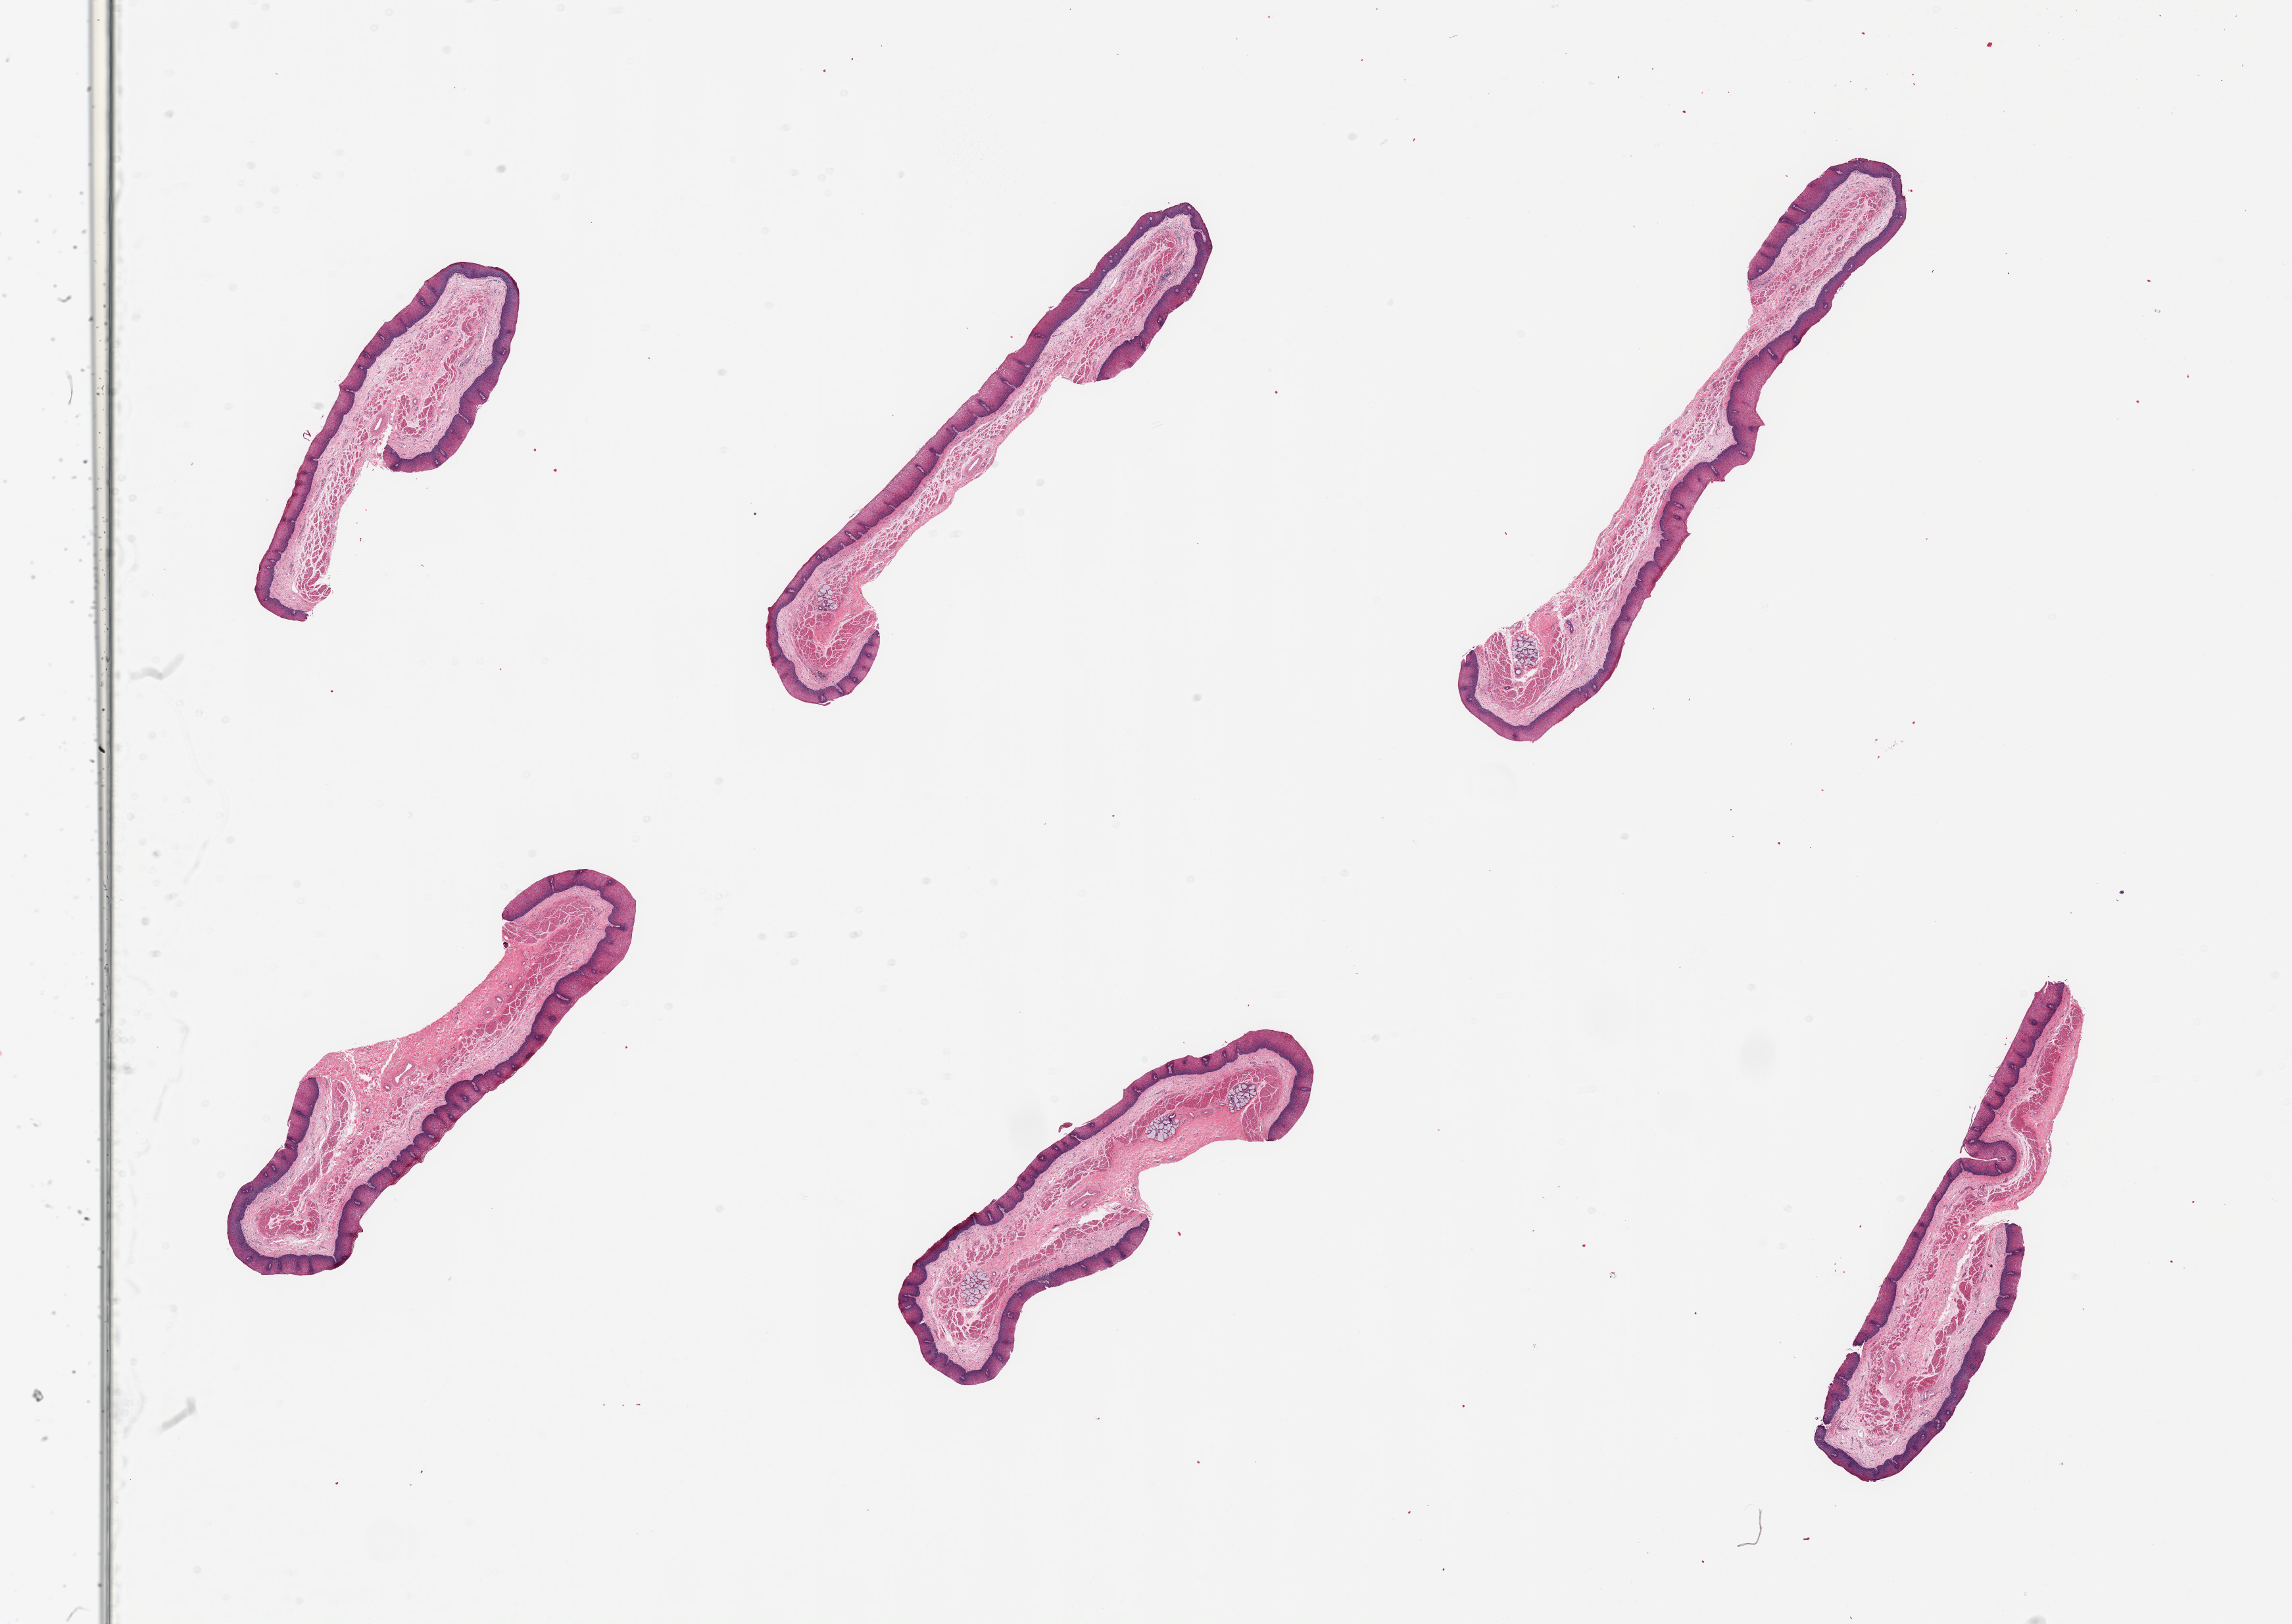
Digitized haematoxylin and eosin-stained section — shown as a low-resolution overview of the whole scanned area (about 27.6 x 19.5 mm), PAXgene-fixed, paraffin-embedded tissue, section of esophageal mucous membrane (target tissue), donor tissue sample. Female donor.
- reviewer comment on this tissue sample: 6 pieces; focal submucosal glands in 2 pieces